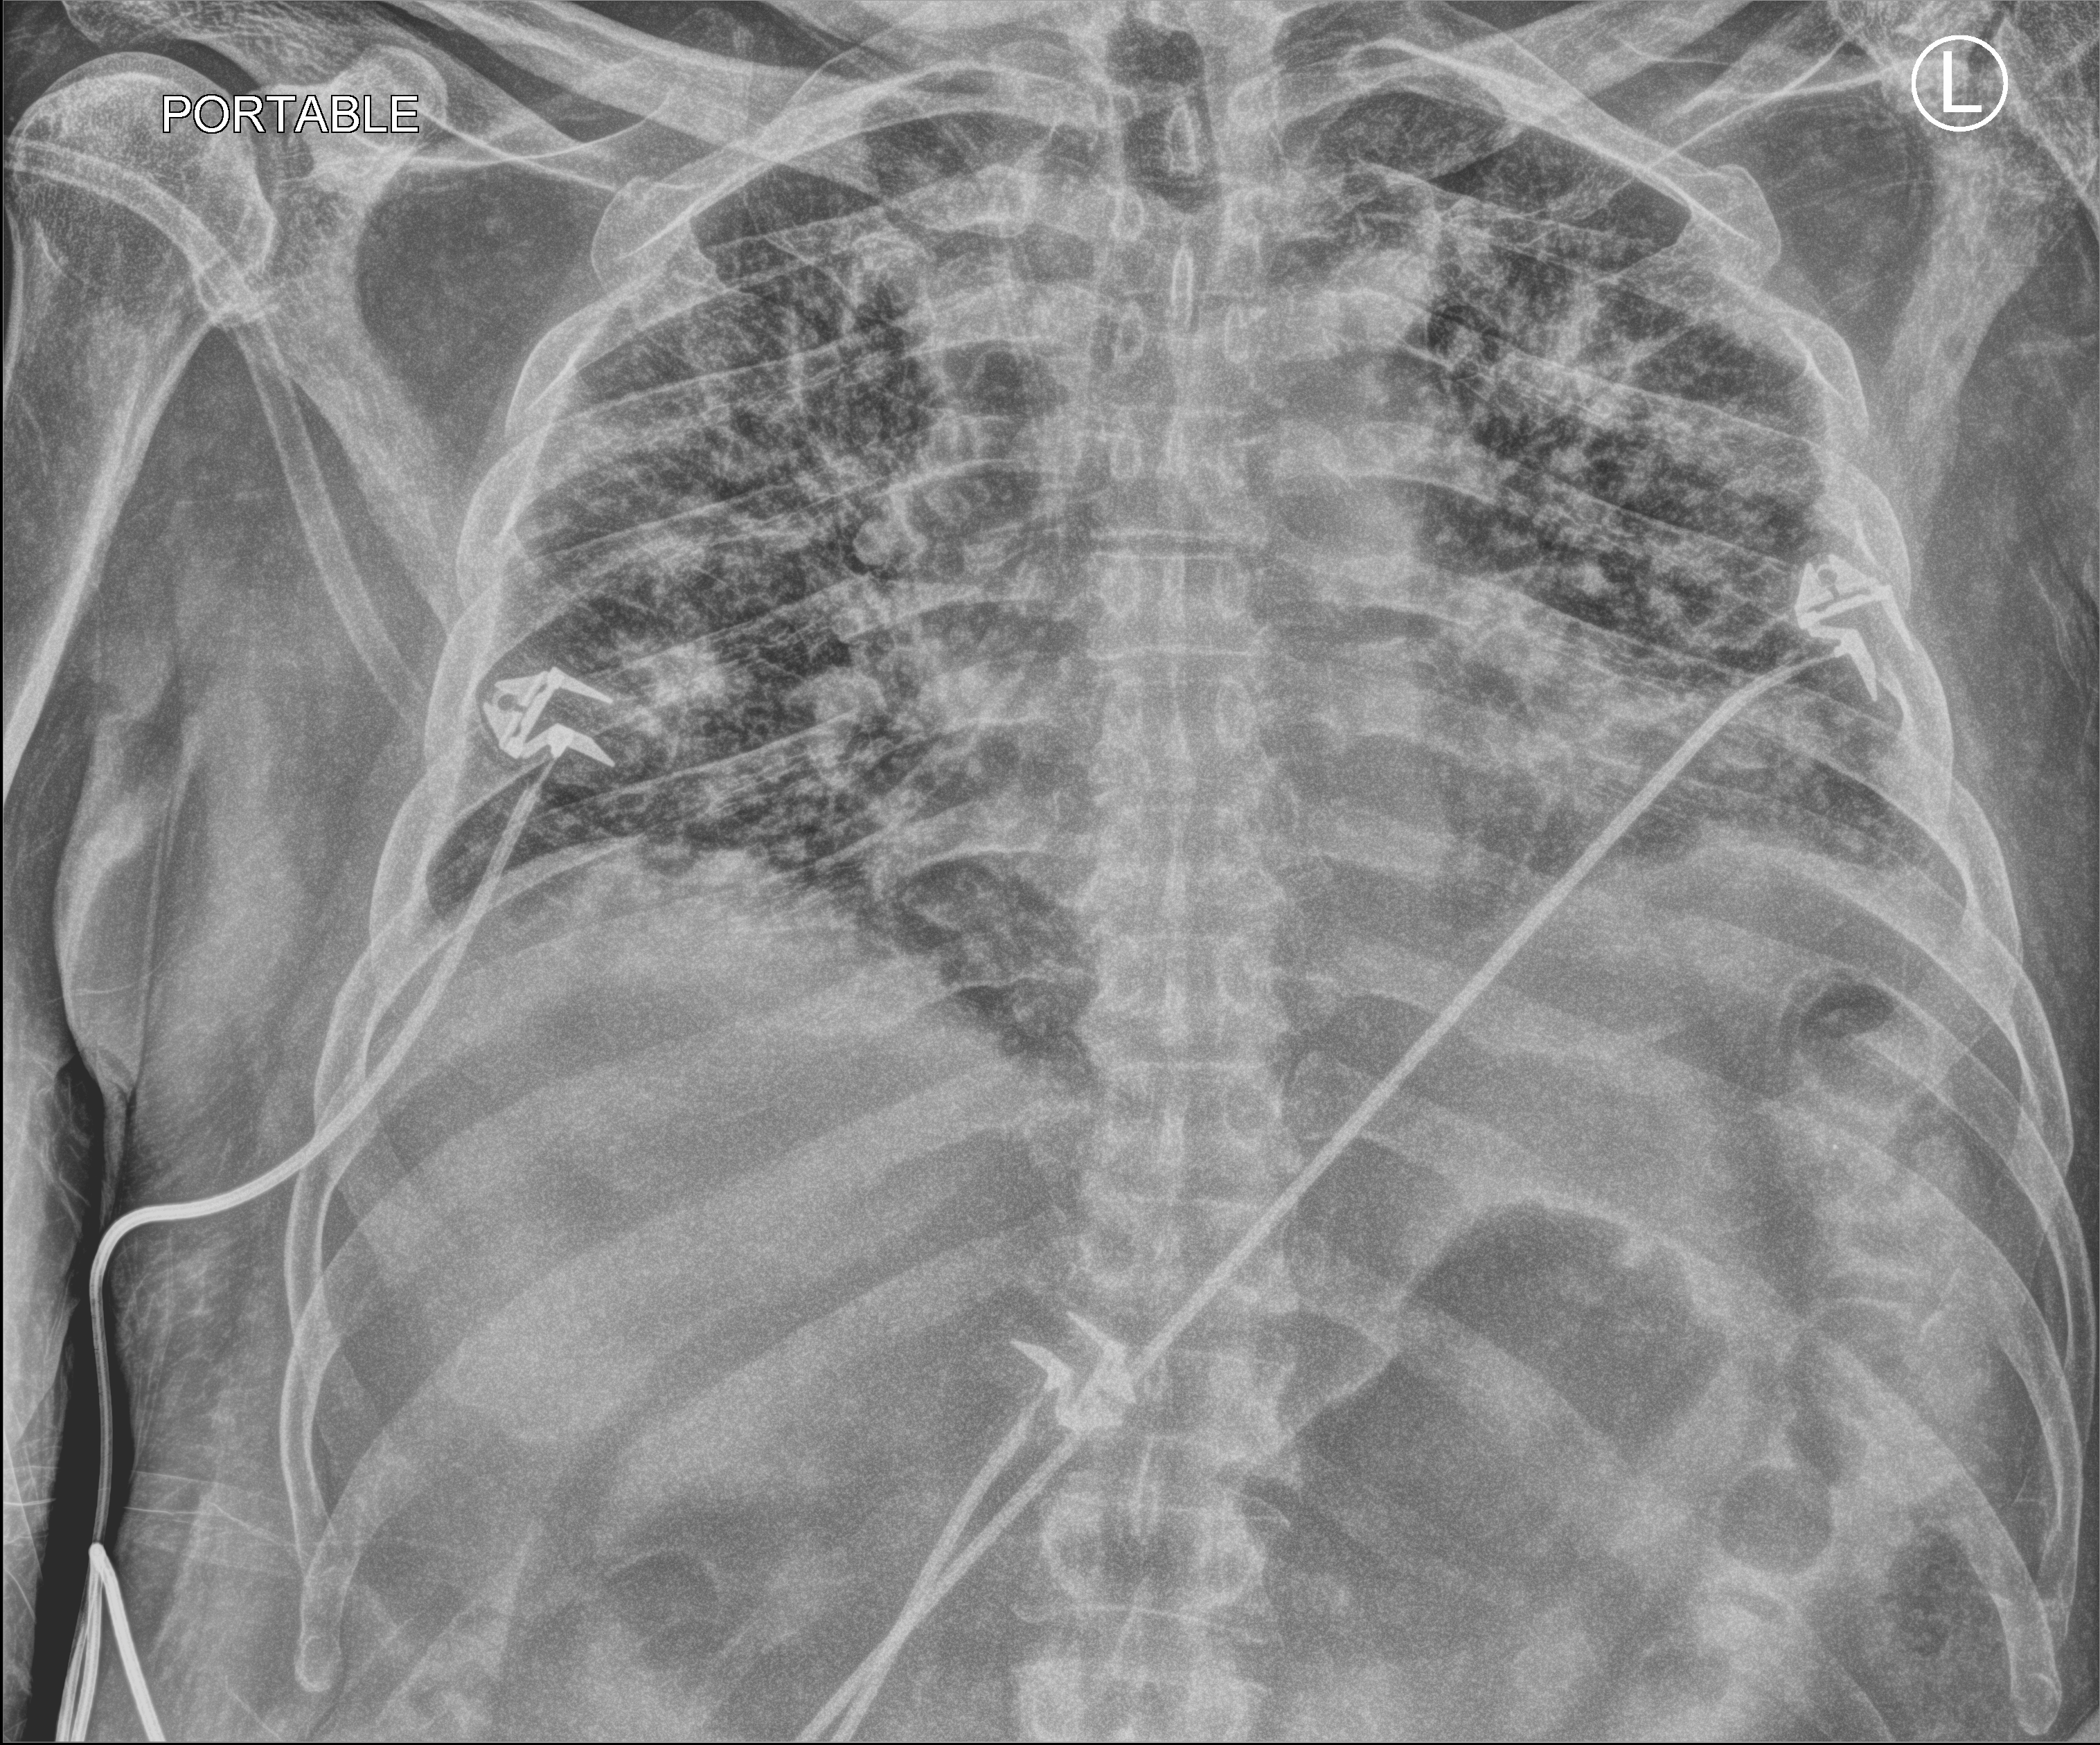
Chest X-ray (portable), anteroposterior (AP) projection. Male patient hospitalised with COVID-19, age 60–74 years.
From the hospital-stay record, not from the radiograph (when in the stay this image was taken is not recorded):
- admitted to intensive care during this hospital stay: no
- mechanically ventilated during this hospital stay: no